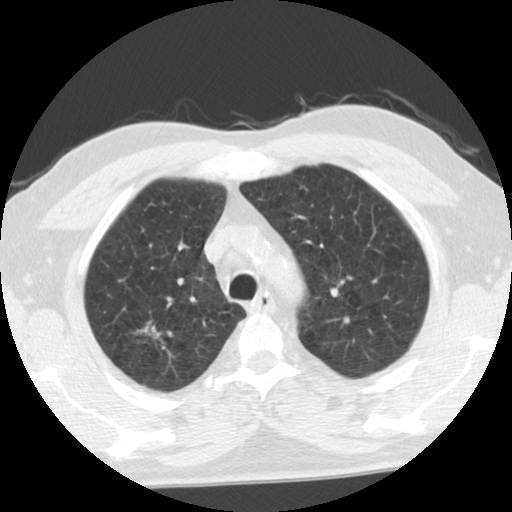
Low-dose screening chest CT, one axial slice; position 89 of 116 along the scan axis; lung window (W 1500 / L -600 HU); 2.5 mm slice thickness; 512 × 512 image matrix.
Annotated regions visible in this slice (expert manual segmentation):
- lesion 1 (tumor, upper lobe of right lung): bounding box [x1, y1, x2, y2] px = [134, 322, 162, 339]